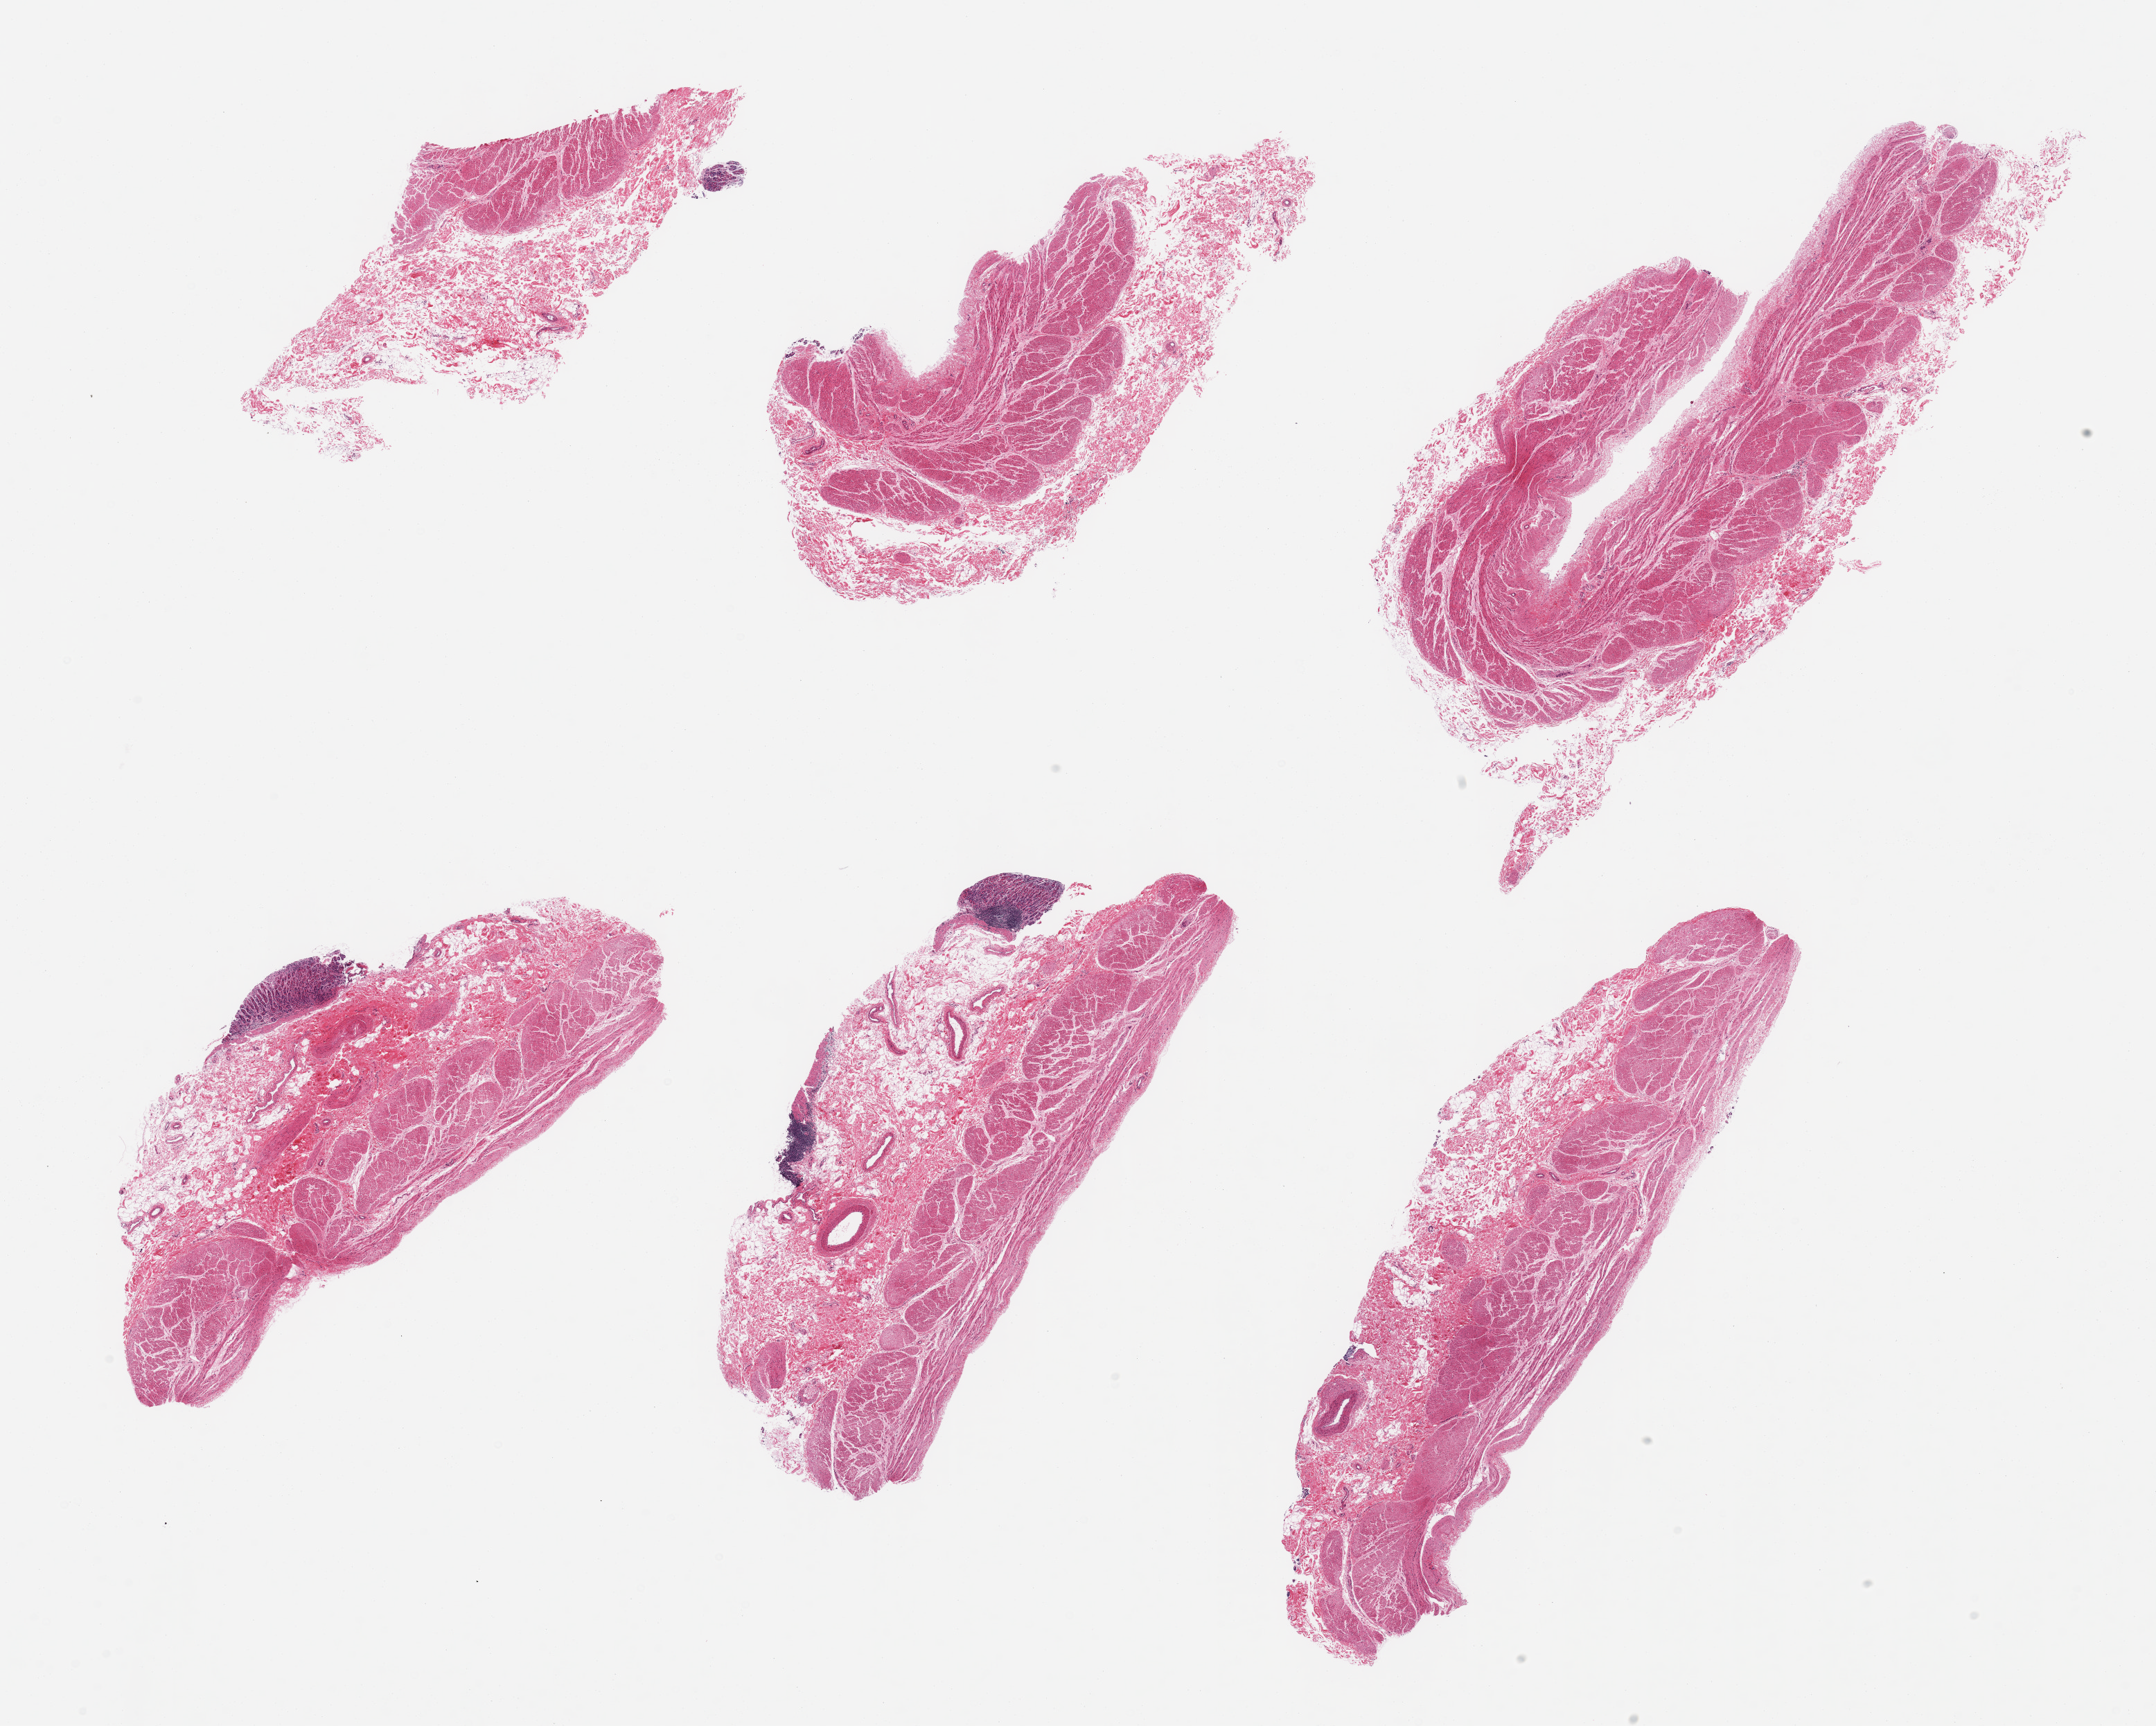
Digitized hematoxylin and eosin (H&E)-stained section — a low-resolution overview of the entire scanned area, about 24.6 x 19.7 mm, PAXgene-fixed paraffin-embedded (PFPE) section, target tissue: stomach, donor tissue sample. Donor: male.
Reviewer comment on this tissue sample: 6 pieces, target mucosa partly sloughed, up to ~0.5mm, moderately autolyzed.